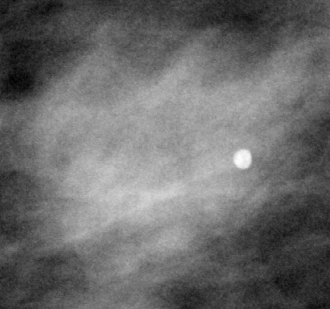
Region of interest cut from a scanned film mammogram (one marked finding), right breast, MLO view, BI-RADS breast density category 2 (scale 1–4).
Finding: mass, shape asymmetric breast tissue; BI-RADS assessment category 2; subtlety rating 5 on a 1 (subtle) to 5 (obvious) scale; benign; no additional work-up was recommended (benign without callback).